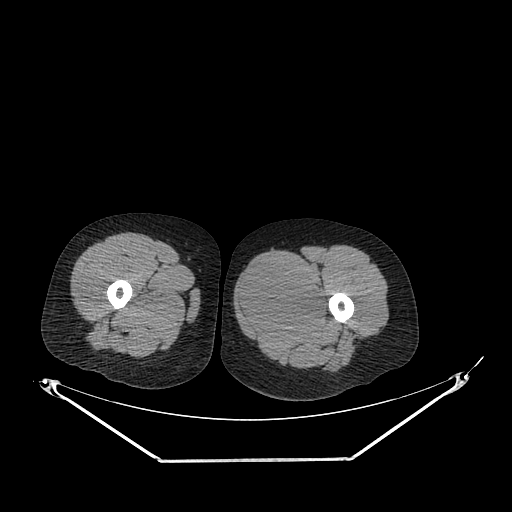
CT of an extremity soft-tissue mass (from a PET/CT study), one axial slice. Slice 234 of 267 in the series (ordered by position). Soft-tissue window (W 400 / L 40 HU). 3.75 mm slice thickness. 512 × 512 image matrix, field of view 500 × 500 mm. Female patient. From the clinical record (not read from this slice): histological type: pleiomorphic leiomyosarcoma; grade: intermediate; site of the primary tumour: left thigh.
Annotated regions visible in this slice (expert contour drawn on MRI and transferred to this co-registered scan by the dataset authors):
- gross tumour volume including surrounding oedema: bounding box [x1, y1, x2, y2] px = [237, 263, 332, 336]
- gross tumour volume (mass): [237, 263, 328, 332]